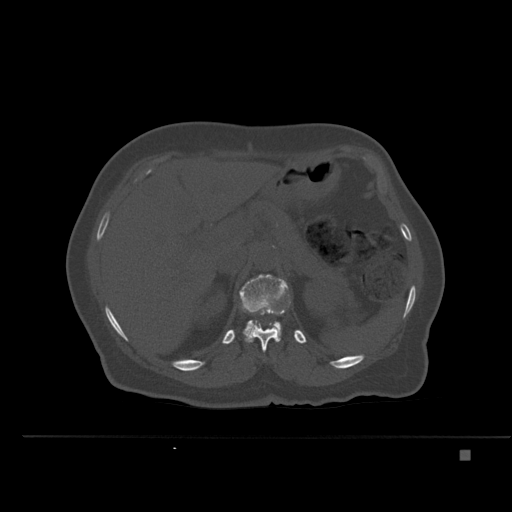
CT including the spine, one axial slice; slice 248 of 477 in the series (ordered by position); bone window (W 1800 / L 400 HU); 1.5 mm slice thickness; 512 × 512 image matrix, field of view 422 × 422 mm. Female patient, age 74 years. From the clinical record (not read from this slice): primary cancer: colon.
Outlined on this slice (semi-automatic segmentation, software-assisted and operator-edited):
- L1 vertebra: box from (x=239, y=274) to (x=290, y=342) px
- T12 vertebra: (x=243, y=301)–(x=290, y=352)